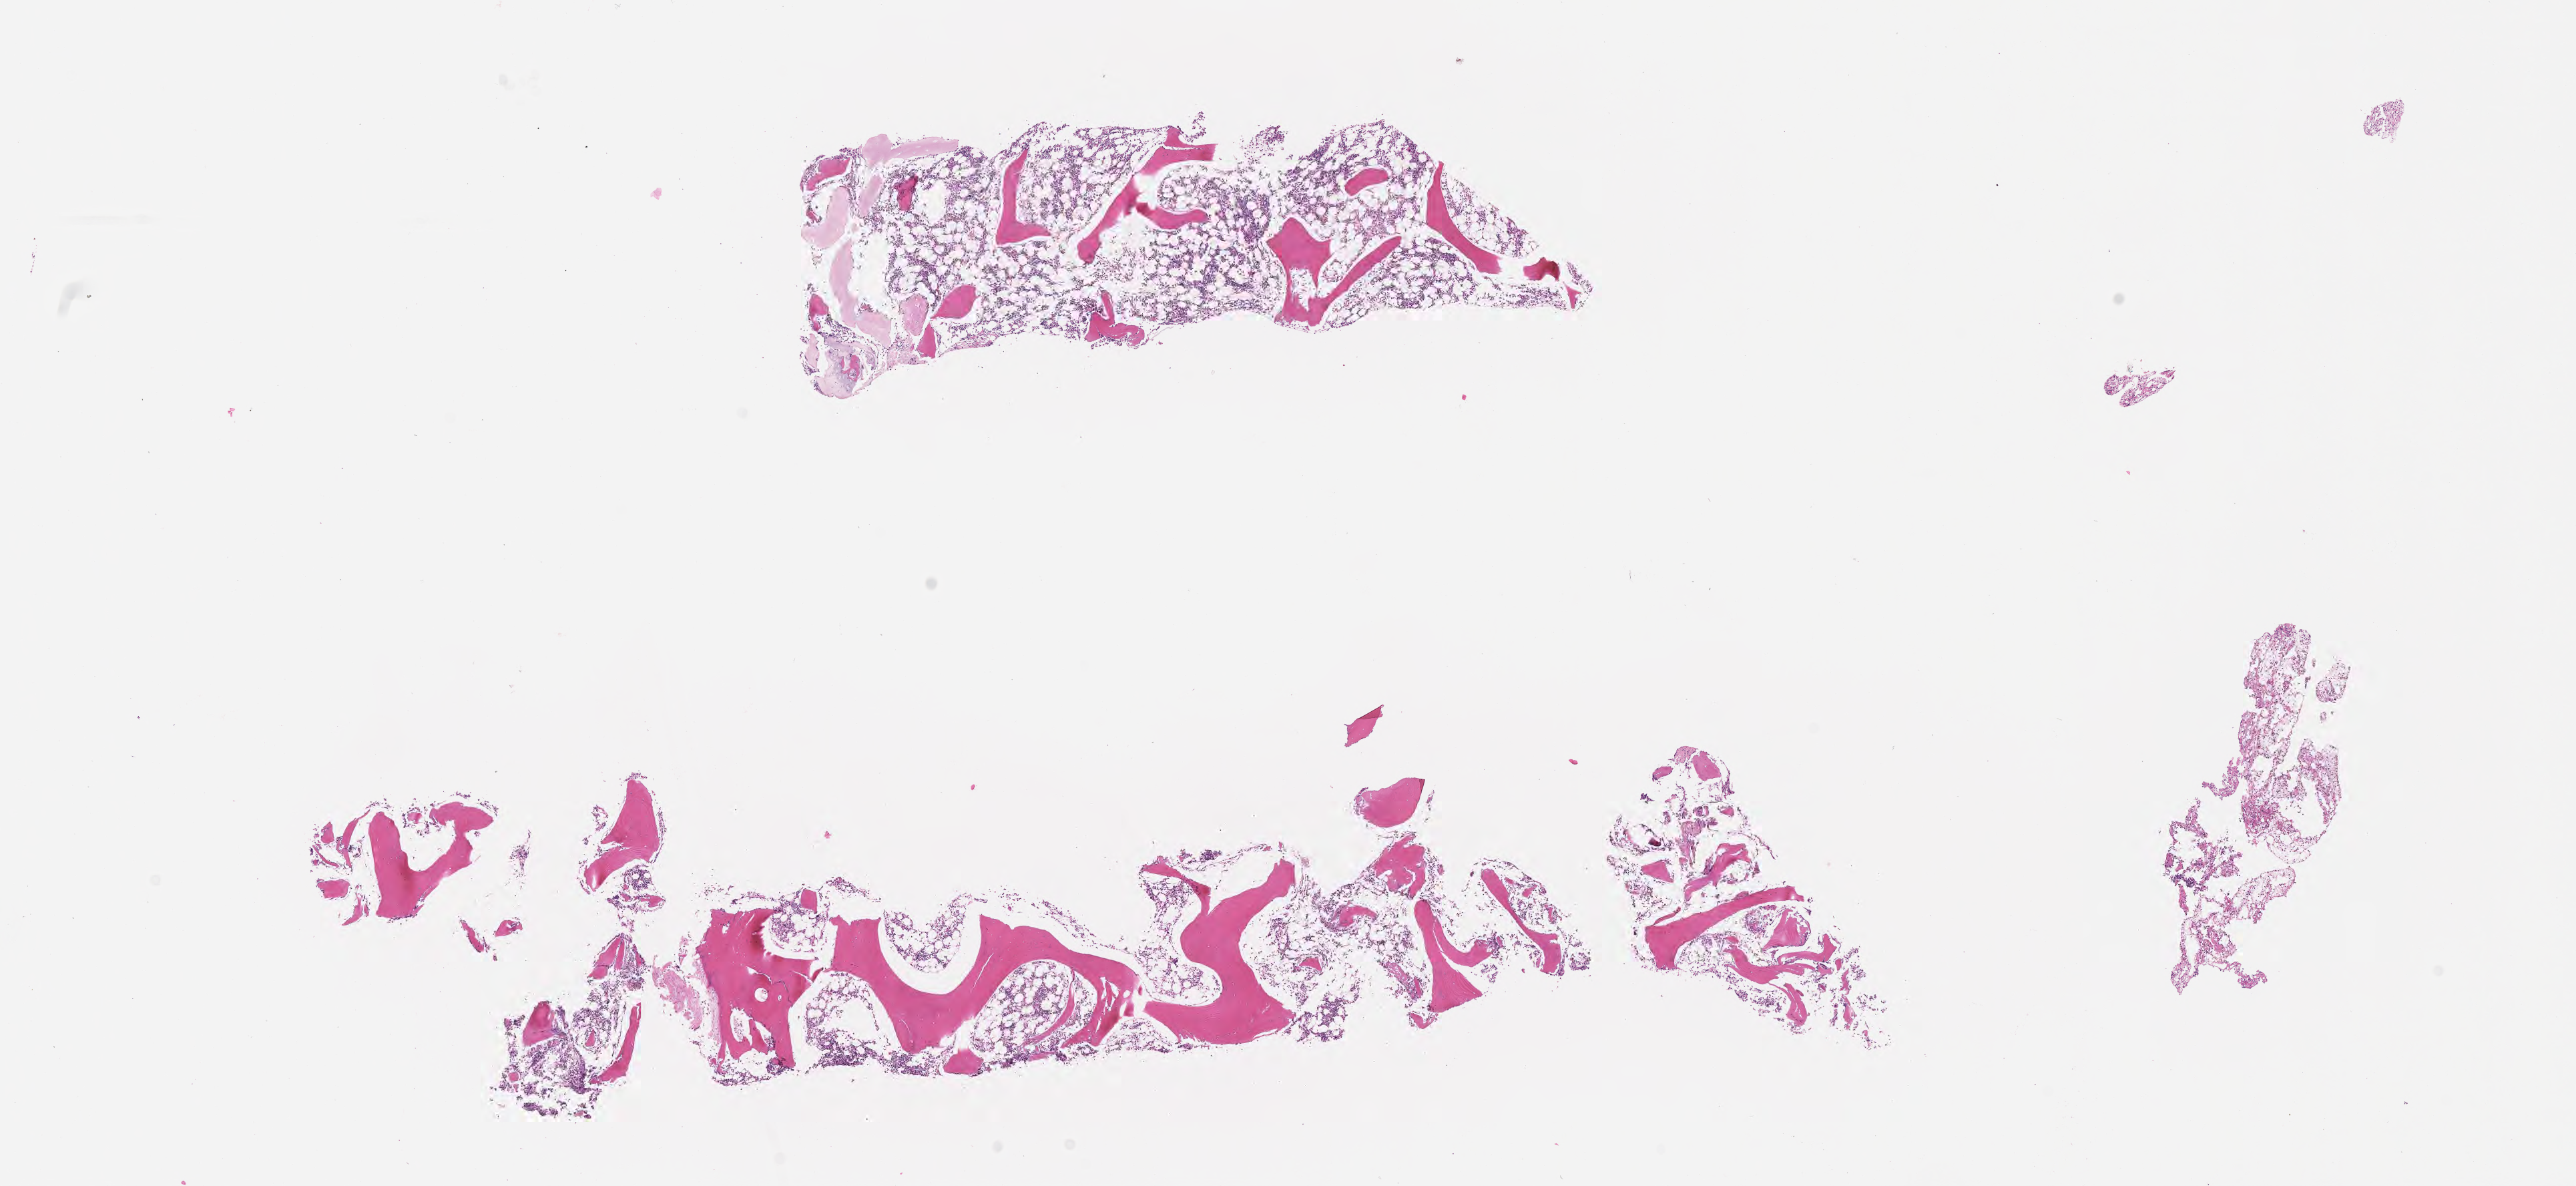
Digitized hematoxylin and eosin (H&E)-stained section — a low-resolution overview of the entire scanned area, about 15.6 x 7.2 mm. Formalin-fixed paraffin-embedded section. Normal-tissue sample (non-tumor) from a patient with burkitt lymphoma, NOS. Male, age 9 years at initial diagnosis. Slide review estimates, as recorded: tumor cells 0%, tumor nuclei 0%, stromal cells 0%, necrosis 0%, normal cells 100%. Infiltration values recorded for this section: lymphocyte infiltration 10%, monocyte infiltration 10%, neutrophil infiltration 50%.
This section: non-tumor tissue sample; the patient's diagnosis is given above. Section: top of the tissue portion.